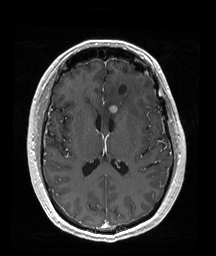
Brain MRI from a brain-tumour surgery series, one axial slice; slice 89 of 192 in the series (ordered by position); T1-weighted post-contrast; 1 mm slice thickness; 216 × 256 image matrix, field of view 211 × 250 mm. Case-level facts recorded for this patient, not image findings: histopathology: Oligodendroglioma; WHO grade: 2; IDH mutation: yes; tumour location: Left Frontal (septal).
Annotated regions visible in this slice (outlined manually by an expert reader):
- tumour: bounding box <109,105,118,113> (left, top, right, bottom; pixels)